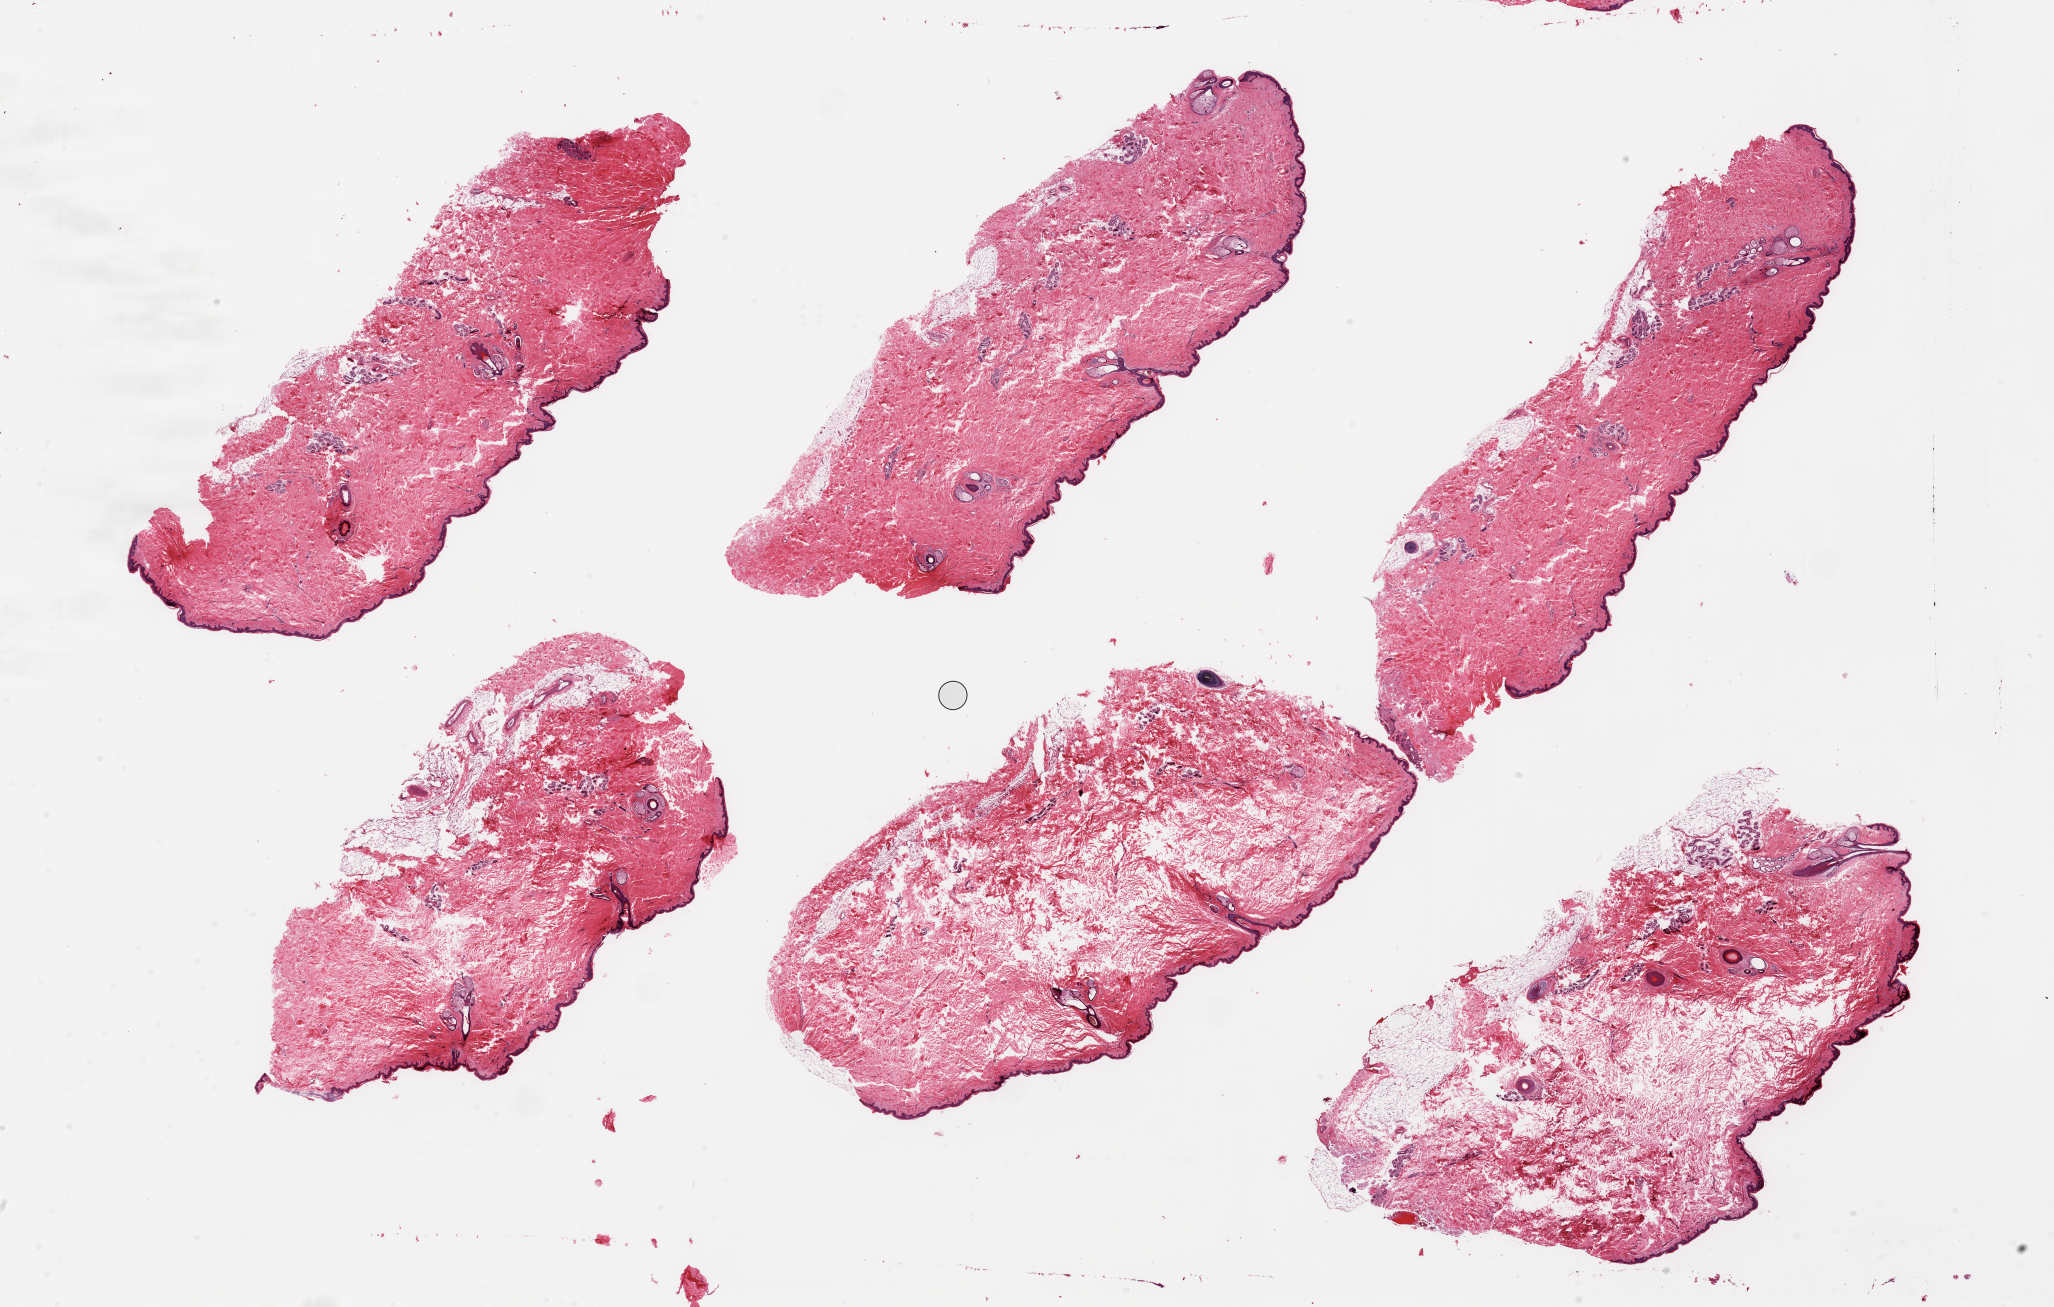
Digitized haematoxylin and eosin-stained section — shown as a low-resolution overview of the whole scanned area (about 32.5 x 20.7 mm, from a 20x scan); PAXgene-fixed paraffin-embedded (PFPE) section; section of skin of suprapubic region (target tissue); tissue donor sample. Male donor.
Pathologist's review note for this sample: 6 pieces; includes up to ~10% mostly attached fat.